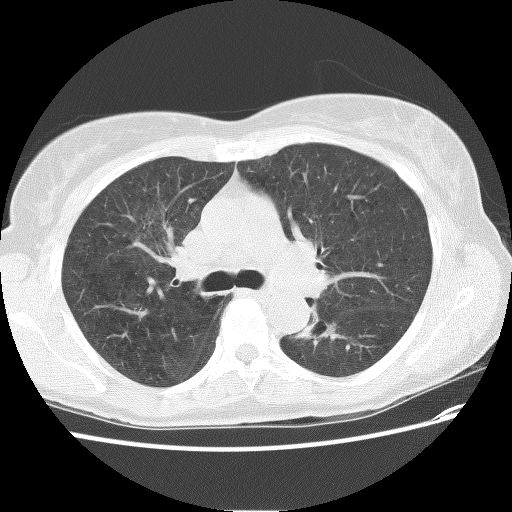
Low-dose screening chest CT, axial slice; first (baseline) screen; lung window (W 1500 / L -600 HU); 120 kVp; slice 41 of 118 in the series. Female participant, aged 62 years at enrolment. Former smoker at enrolment.
• Expert-annotated lung lesion, bounding box (x1, y1, x2, y2) in pixels: (290, 304, 341, 344).
• No non-calcified nodule or mass ≥4 mm was recorded by the screening reader at this exam.
• Official screen result: negative screen, minor abnormalities not suspicious for lung cancer.
• Participant outcome: lung cancer diagnosed 898 days after this screen — squamous cell carcinoma, NOS, left lower lobe, stage IIIB (AJCC 6th edition), 31 mm at pathology.